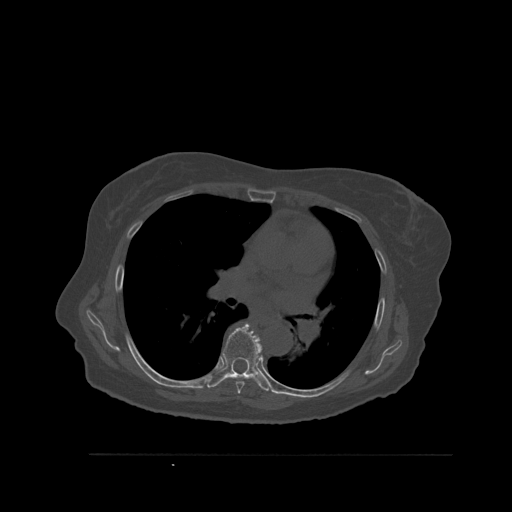
CT including the spine, one axial slice. Slice 371 of 527 in the series (ordered by position). Bone window (W 1800 / L 400 HU). 1.5 mm slice thickness. 512 × 512 image matrix, field of view 470 × 470 mm. Female patient, age 73 years. From the clinical record (not read from this slice): primary cancer: breast.
Structures marked on this image (semi-automatic segmentation, software-assisted and operator-edited):
- T6 vertebra: bounding box <235,359,258,394> (left, top, right, bottom; pixels)
- T7 vertebra: <206,323,270,392>